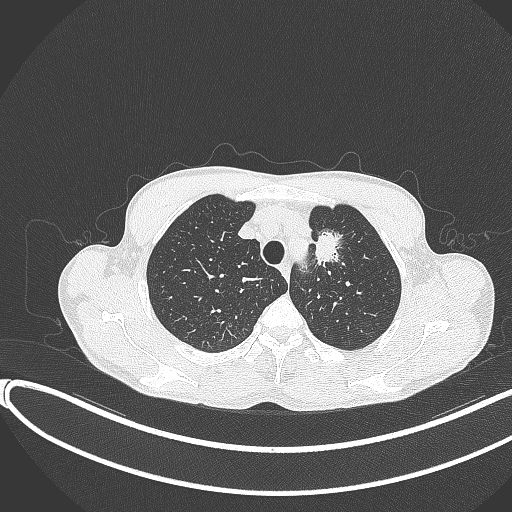
Chest CT, one axial slice; reconstruction kernel B70f; 120 kVp; lung window (W 1500 / L -600 HU); 1 mm slice thickness; 512 × 512 image matrix. Patient: male, 58 years. Case-level facts recorded for this patient, not image findings: clinical TNM (as recorded): T1c N1 M0.
Structures marked on this image (rectangle marked by the reading radiologist):
- lung tumour (recorded histology: adenocarcinoma): box from (x=305, y=226) to (x=350, y=279) px